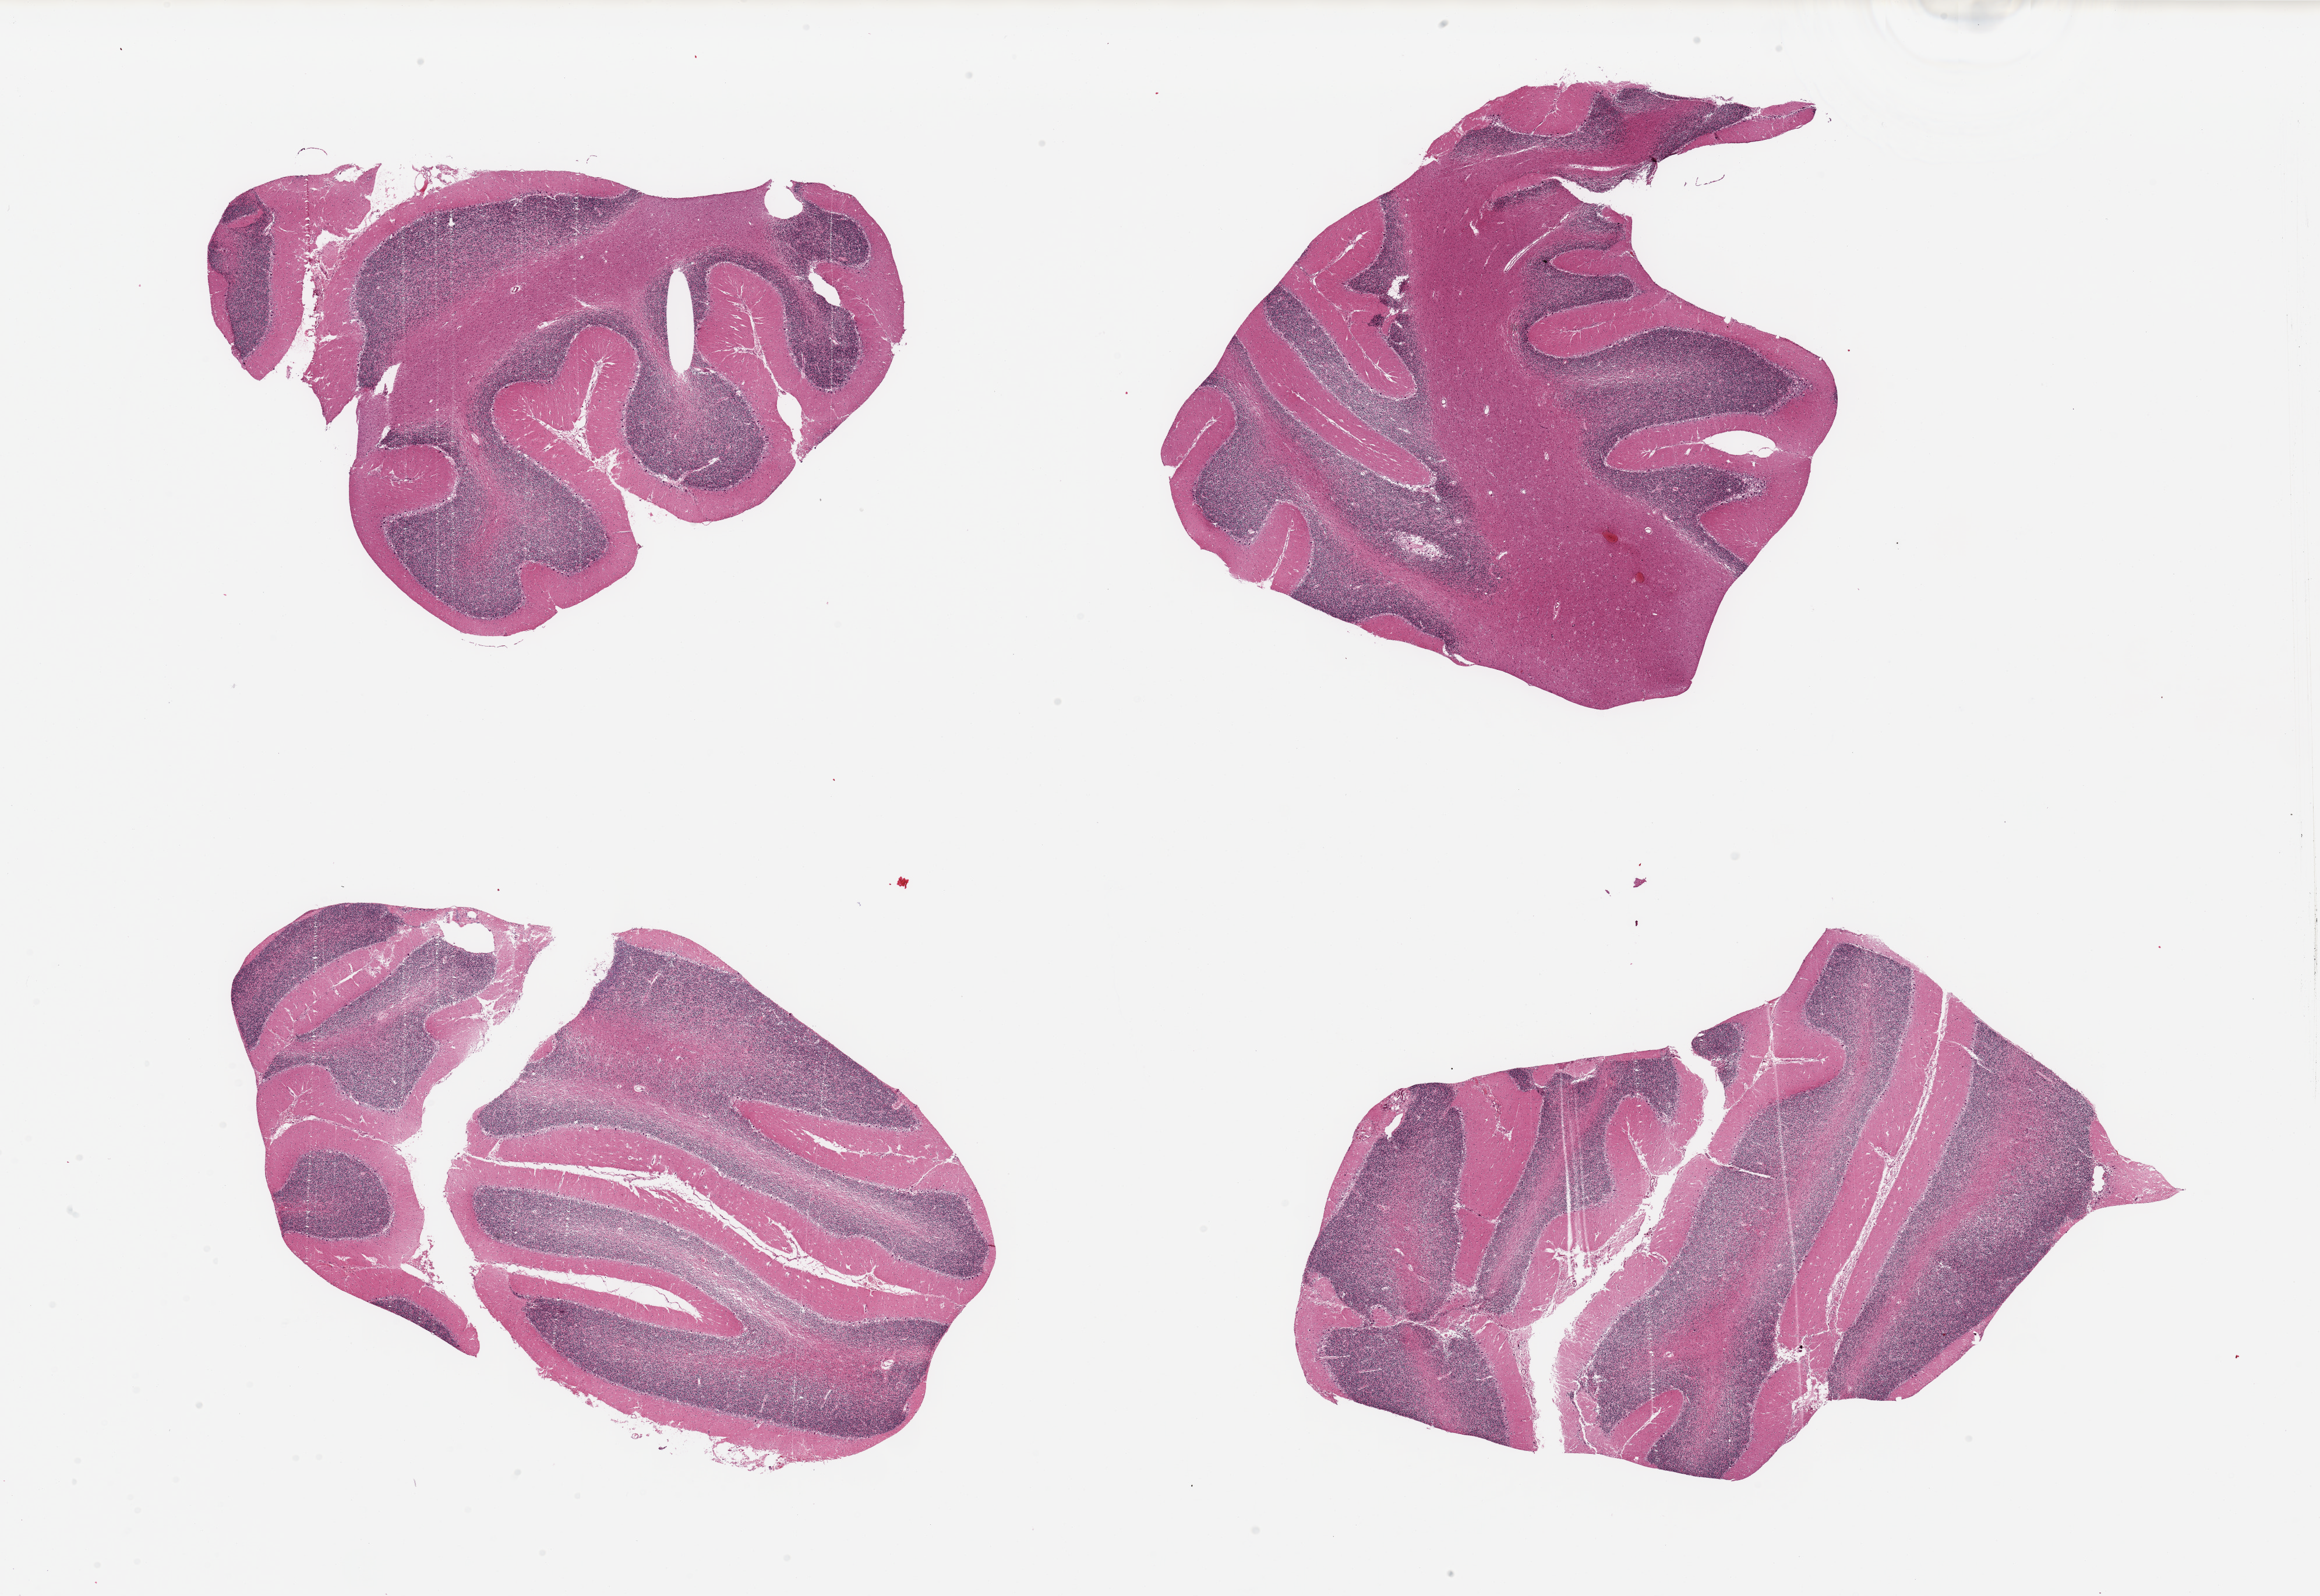
Digitized H&E-stained section, shown as a low-resolution overview of the whole scanned area (about 31.5 x 21.7 mm, slide scanned at 20x); PAXgene-fixed, paraffin-embedded tissue; target tissue: cerebellum; tissue donor sample. Male donor.
Review note (as recorded): 4 pieces, no abnormalities.